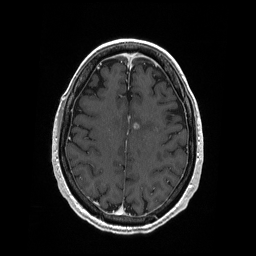
Brain MRI from a brain-tumour surgery series, one axial slice. Slice 72 of 208 in the series (ordered by position). T1-weighted post-contrast. 256 × 256 image matrix, field of view 256 × 256 mm. From the clinical record (not read from this slice): histopathology: Primary diffuse large B-cell lymphoma.
Annotated regions visible in this slice (manually delineated by an expert):
- tumour: bounding box [x1, y1, x2, y2] px = [133, 121, 158, 130]